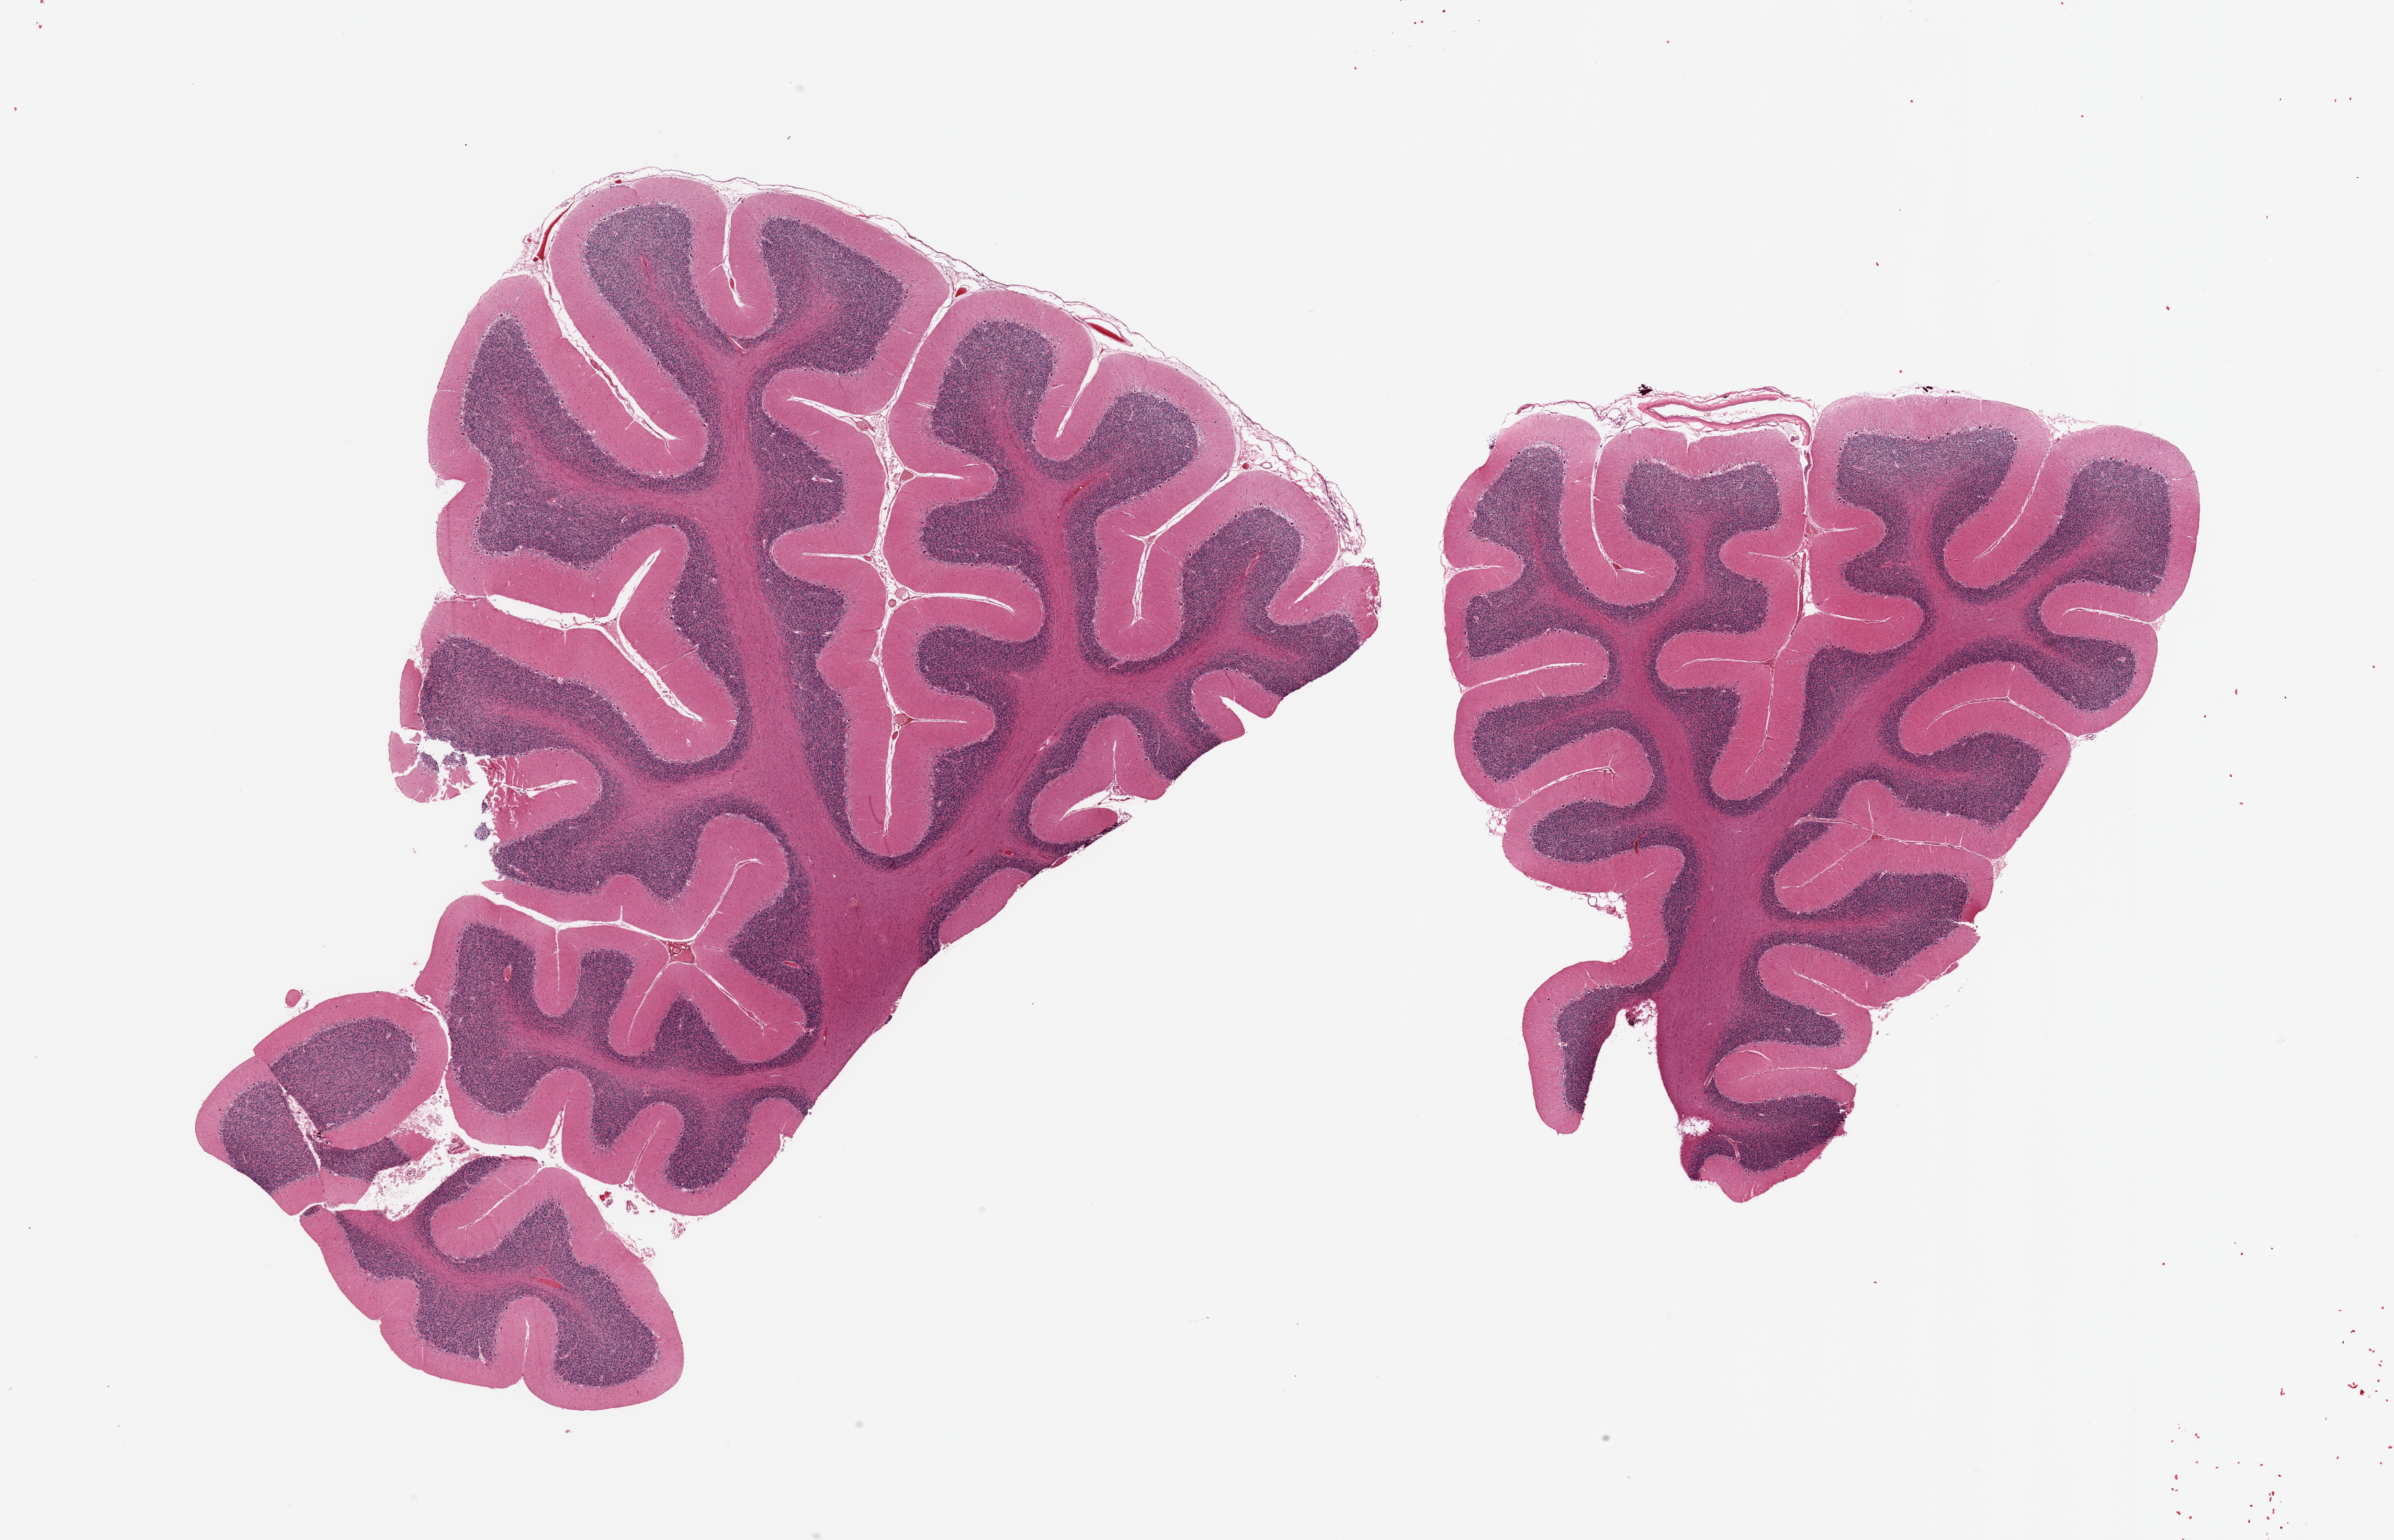
Haematoxylin and eosin whole-slide image, brightfield, a low-resolution overview of the entire scanned area, about 27.6 x 17.7 mm (slide scanned at 20x); PAXgene-fixed, paraffin-embedded tissue; target tissue: cerebellum; tissue donor sample. Donor: male.
Review note (as recorded): 2 pieces; focal meninges; Purkinje cells present.